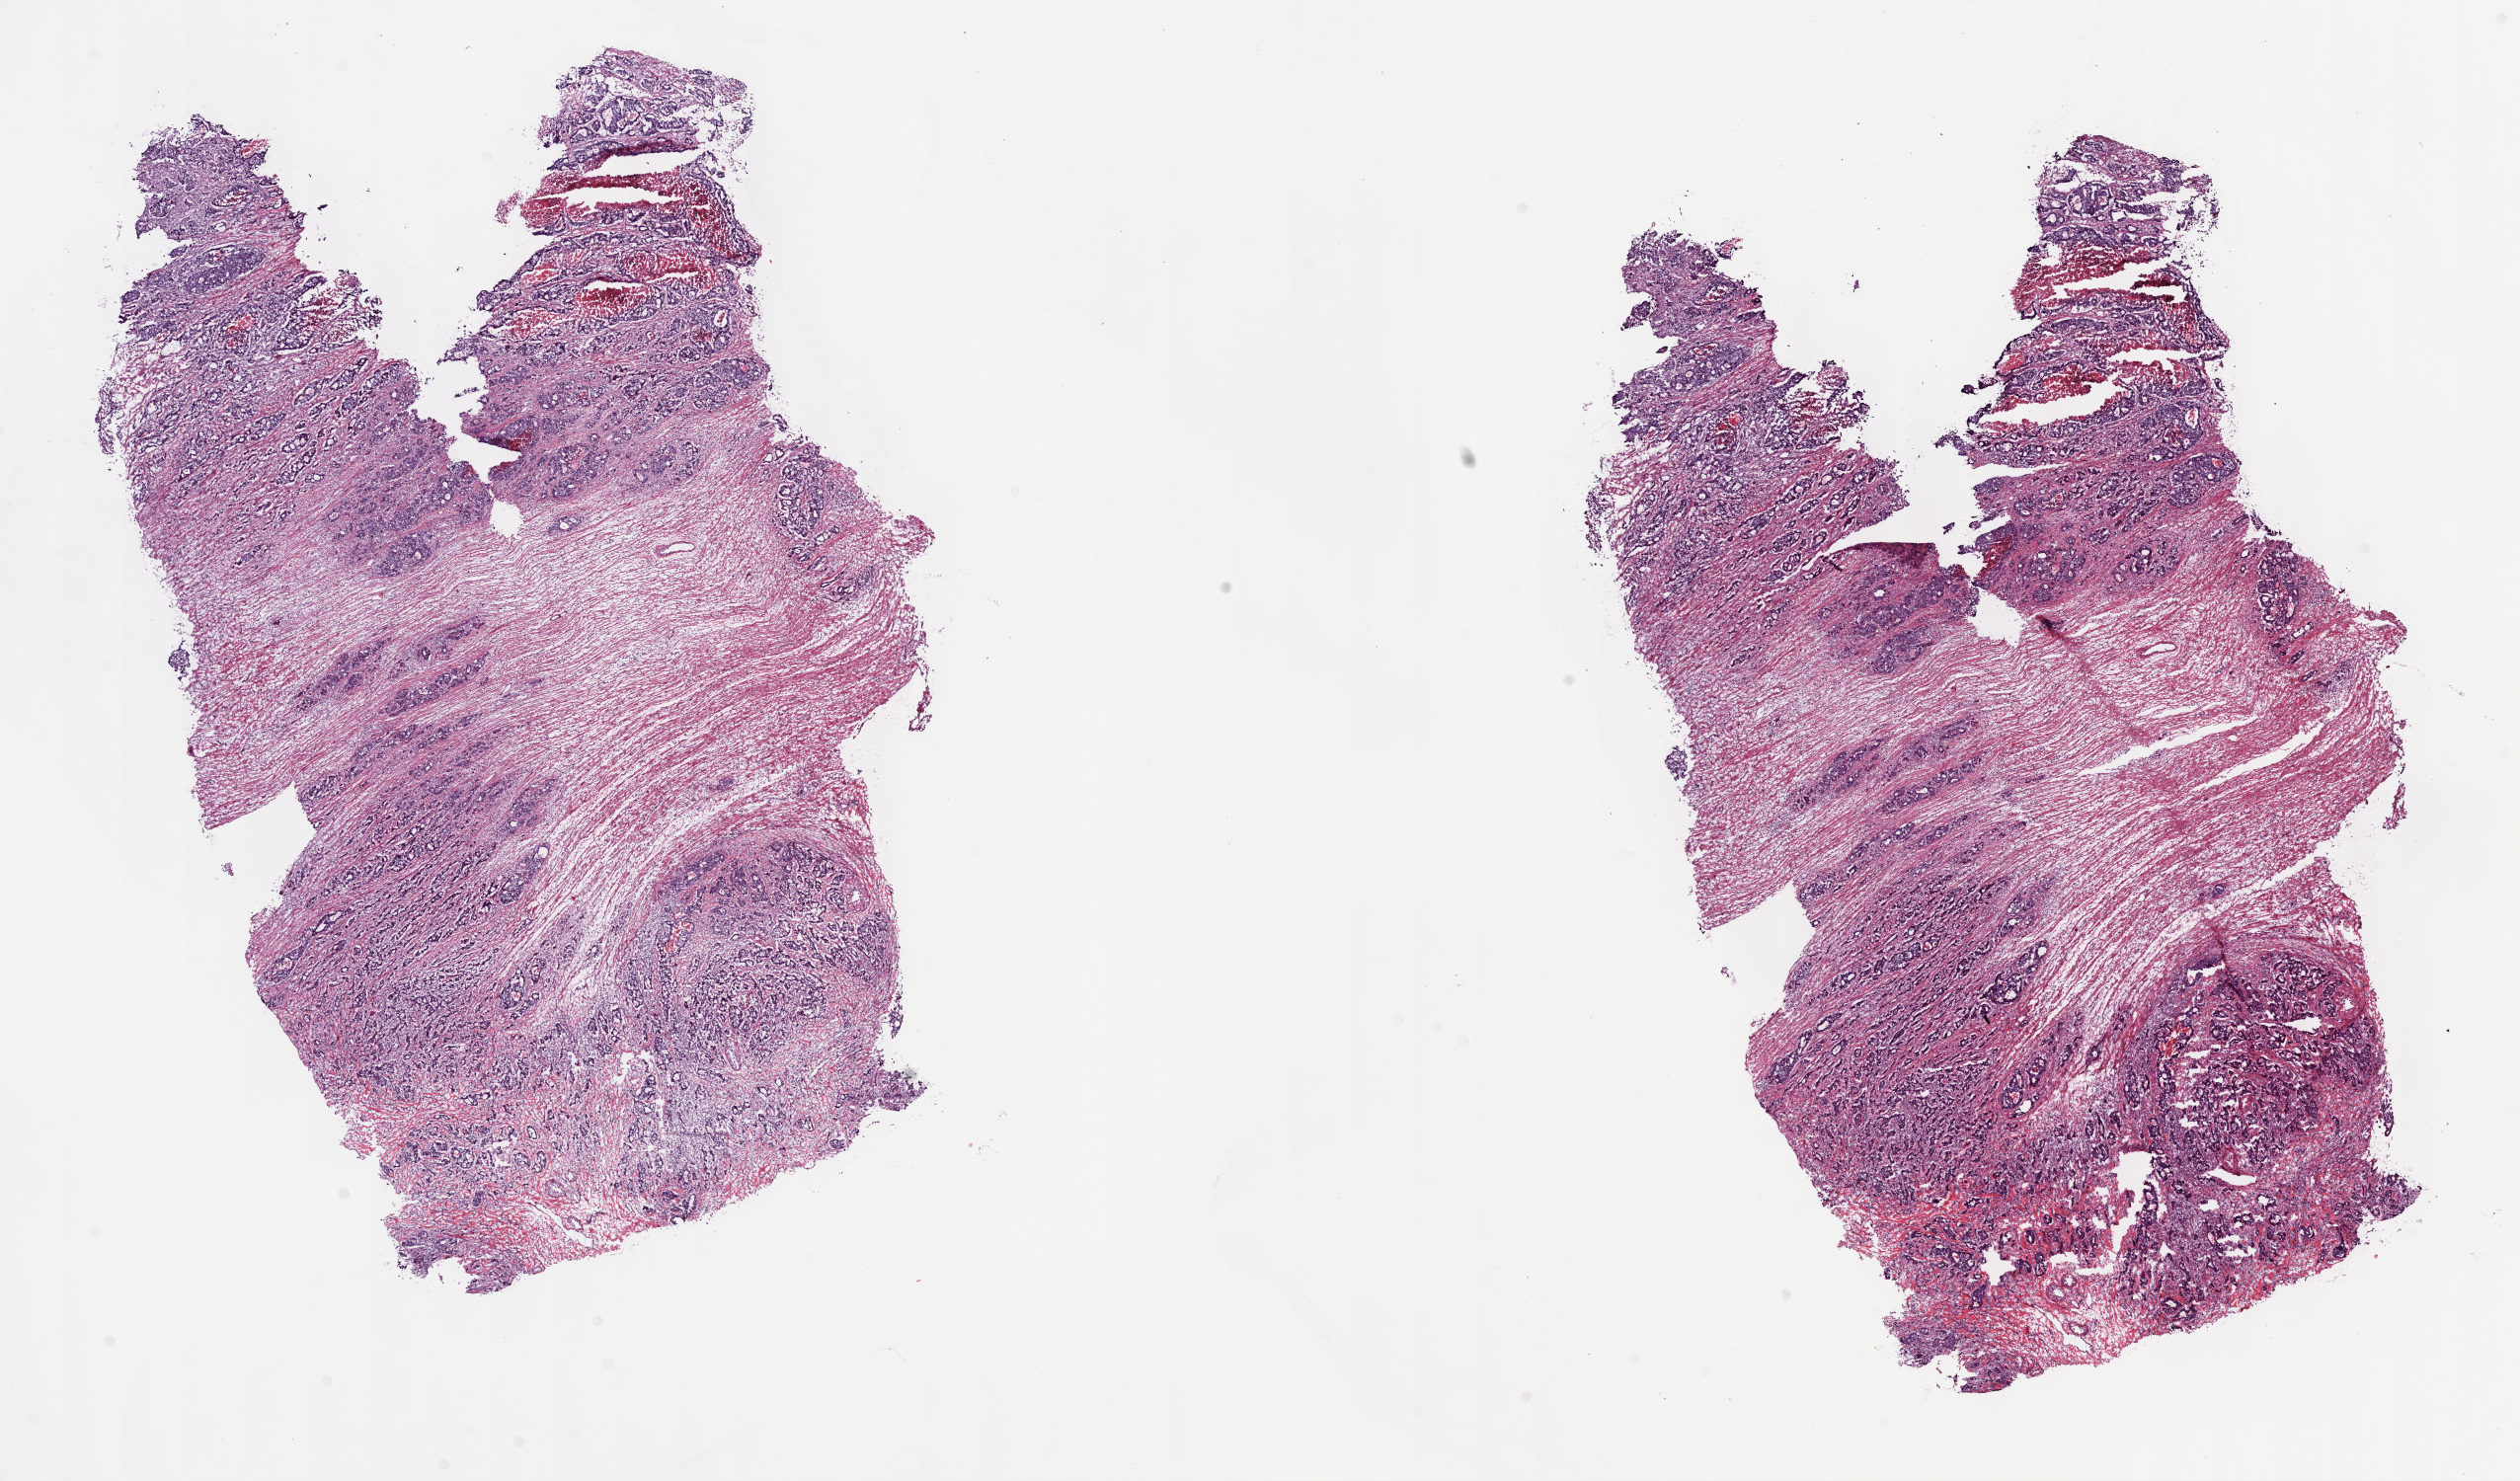
H&E whole-slide image — a low-resolution overview of the entire scanned area, about 20.6 x 12.1 mm, frozen section from the top of the tissue portion, primary tumour sample from the colon. Male, age 79 years at initial diagnosis. Composition of this section per pathologist review: tumour cells 40%, tumour nuclei 85%, normal cells 0%, stromal cells 48%, necrosis 12%. Inflammatory infiltration, as recorded: lymphocyte infiltration 8%, monocyte infiltration 1%, neutrophil infiltration 2%.
Diagnosis: Adenocarcinoma, NOS (ascending colon). AJCC pathologic stage: IV (7th edition). Lymph nodes positive (case pathology): 15 of 22 examined. TNM: T4a N2b M1.